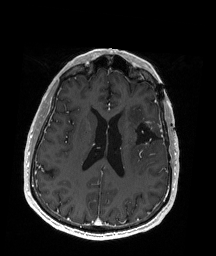
Brain MRI from a brain-tumour surgery series, one axial slice; slice 80 of 192 in the series (ordered by position); T1-weighted post-contrast; 216 × 256 image matrix, field of view 211 × 250 mm. From the clinical record (not read from this slice): histopathology: Oligodendroglioma; WHO grade: 2; IDH mutation: yes; tumour location: Left Insular.
Structures marked on this image (manually delineated by an expert):
- previous resection cavity: bounding box (x1, y1, x2, y2) in pixels: (132, 121, 163, 148)